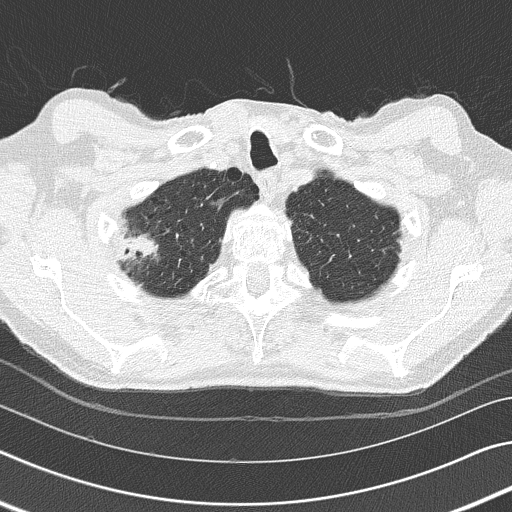
Low-dose screening chest CT, one axial slice; slice 143 of 155 in the series (ordered by position); reconstruction kernel B50f; lung window (W 1500 / L -600 HU); 512 × 512 image matrix, field of view 340 × 340 mm.
Outlined on this slice (expert manual segmentation):
- lesion 1 (tumor, middle lobe of right lung): box from (x=119, y=232) to (x=158, y=269) px